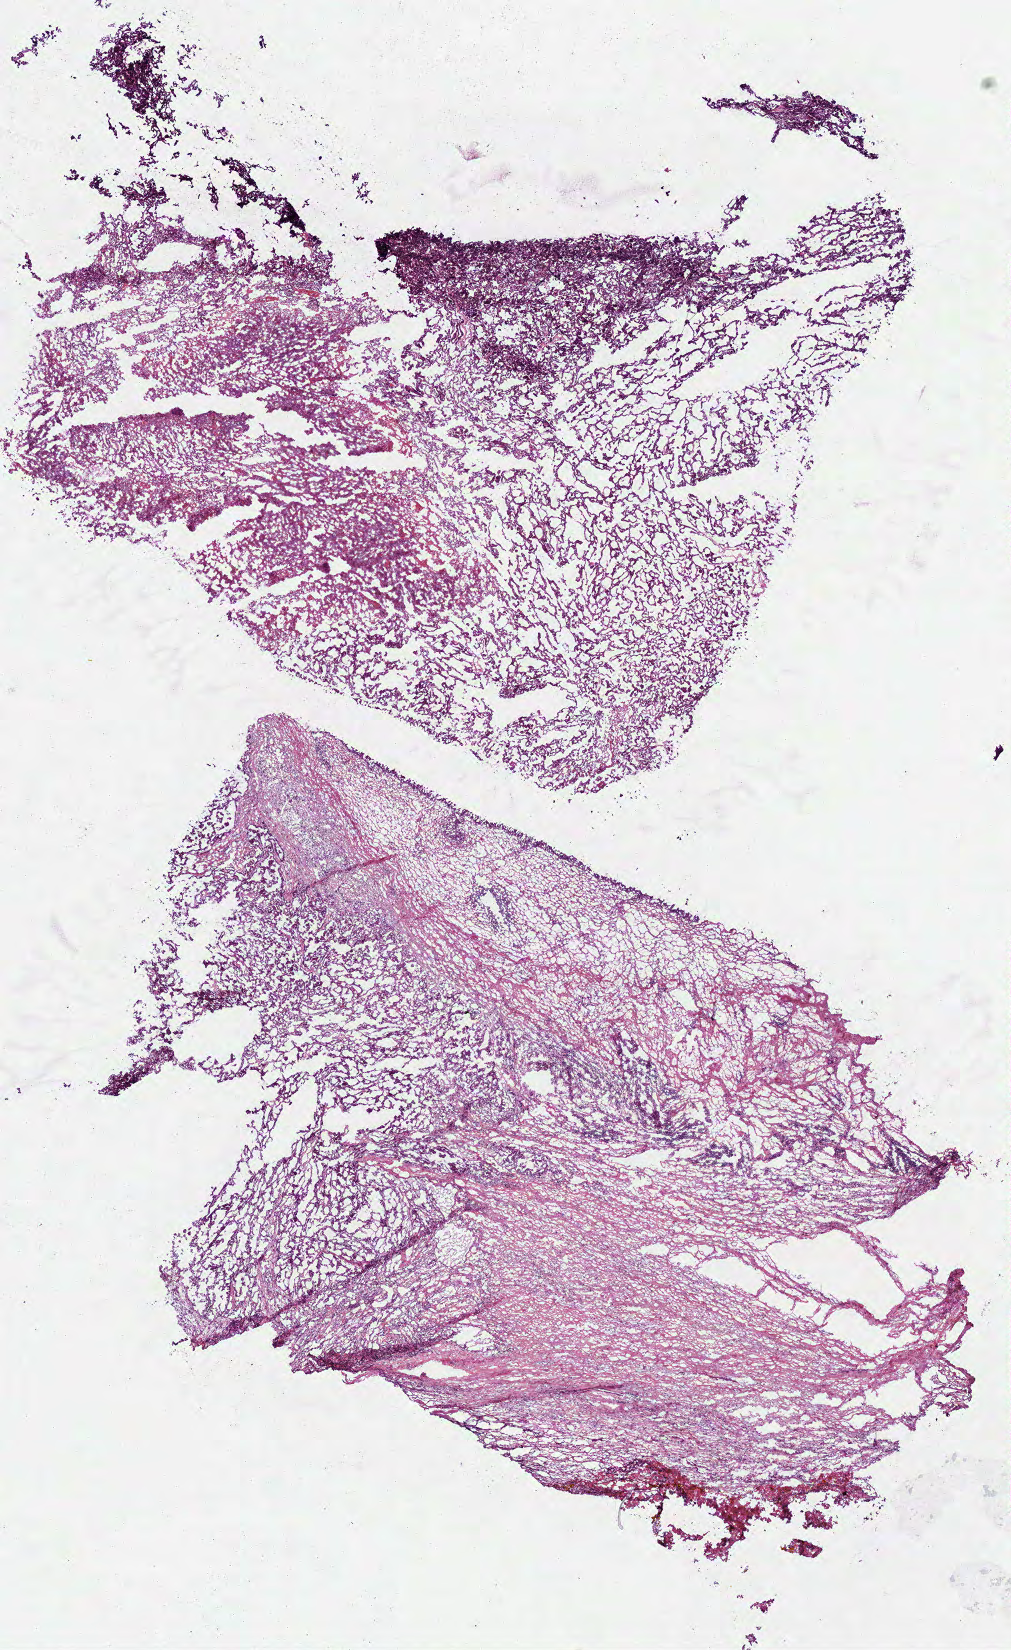
Whole-slide histology image, H&E-stained — low-resolution overview of the scanned area, about 8.0 x 13.0 mm (acquisition: 40x scan); frozen section from the top of the tissue portion; kidney, primary tumour sample. Patient: female, age at initial diagnosis 72 years. Slide review estimates, as recorded: tumour cells 40%, tumour nuclei 65%, normal cells 0%, stromal cells 40%, necrosis 20%.
Diagnosis: Papillary adenocarcinoma, NOS. AJCC pathologic stage: IV. Lymph nodes positive (case pathology): 4 of 14 examined.